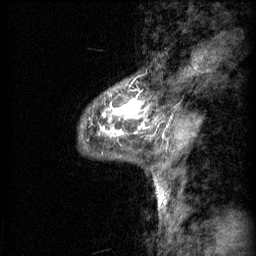
Breast MRI (dynamic contrast-enhanced), one sagittal slice; slice 17 of 60 in the series (ordered by position); 3 images stored at this slice position (order not interpretable as contrast timing); 1.5 T; TE 4.2 ms, TR 11 ms; 2 mm slice thickness; 256 × 256 image matrix. Female patient, age 48 years.
Outlined on this slice (semi-automatically segmented with operator editing):
- analysis volume of interest (the breast-tissue region the enhancement analysis was run in; not a lesion): bounding box <101,86,148,137> (left, top, right, bottom; pixels)
- tumour enhancement mask (voxels above the 70 % enhancement threshold inside the analysis volume of interest): <103,102,143,135>